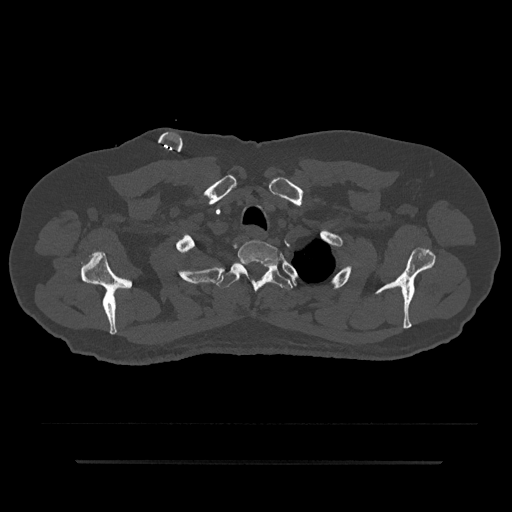
CT including the spine, one axial slice. Slice 713 of 797 in the series (ordered by position). Reconstruction kernel Br40s/3. Bone window (W 1800 / L 400 HU). 512 × 512 image matrix. Male patient, age 59 years. Case-level facts recorded for this patient, not image findings: primary cancer: bile ducts; vertebrae with lytic lesions (as recorded): T10.
Outlined on this slice (semi-automatic segmentation, software-assisted and operator-edited):
- T1 vertebra: bounding box [x1, y1, x2, y2] px = [237, 240, 279, 264]
- T2 vertebra: [216, 262, 292, 293]